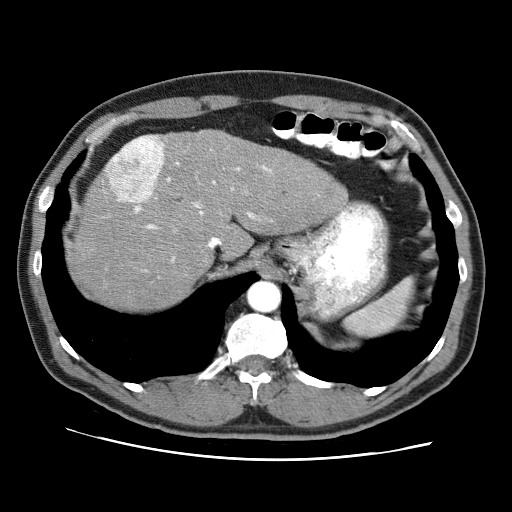
Contrast-enhanced abdominal CT (liver protocol), one axial slice; slice 55 of 71 in the series (ordered by position); soft-tissue window (W 400 / L 40 HU); 2.5 mm slice thickness; 512 × 512 image matrix, field of view 360 × 360 mm. Case-level facts recorded for this patient, not image findings: diagnosis: hepatocellular carcinoma (patient treated with transarterial chemoembolisation; whether this scan precedes or follows treatment is not stated here); TNM stage (as recorded): Stage-II; Child-Pugh class: A; tumour differentiation: well differentiated; tumour size: 4.6 cm.
Annotated regions visible in this slice (semi-automatically segmented with operator editing):
- abdominal aorta: bounding box <248,282,279,310> (left, top, right, bottom; pixels)
- liver parenchyma outside the tumour (the mass and vessels are separate outlines, so this box may not span the whole liver): <72,130,348,310>
- mass: <104,134,164,203>
- liver vessels: <135,163,271,261>